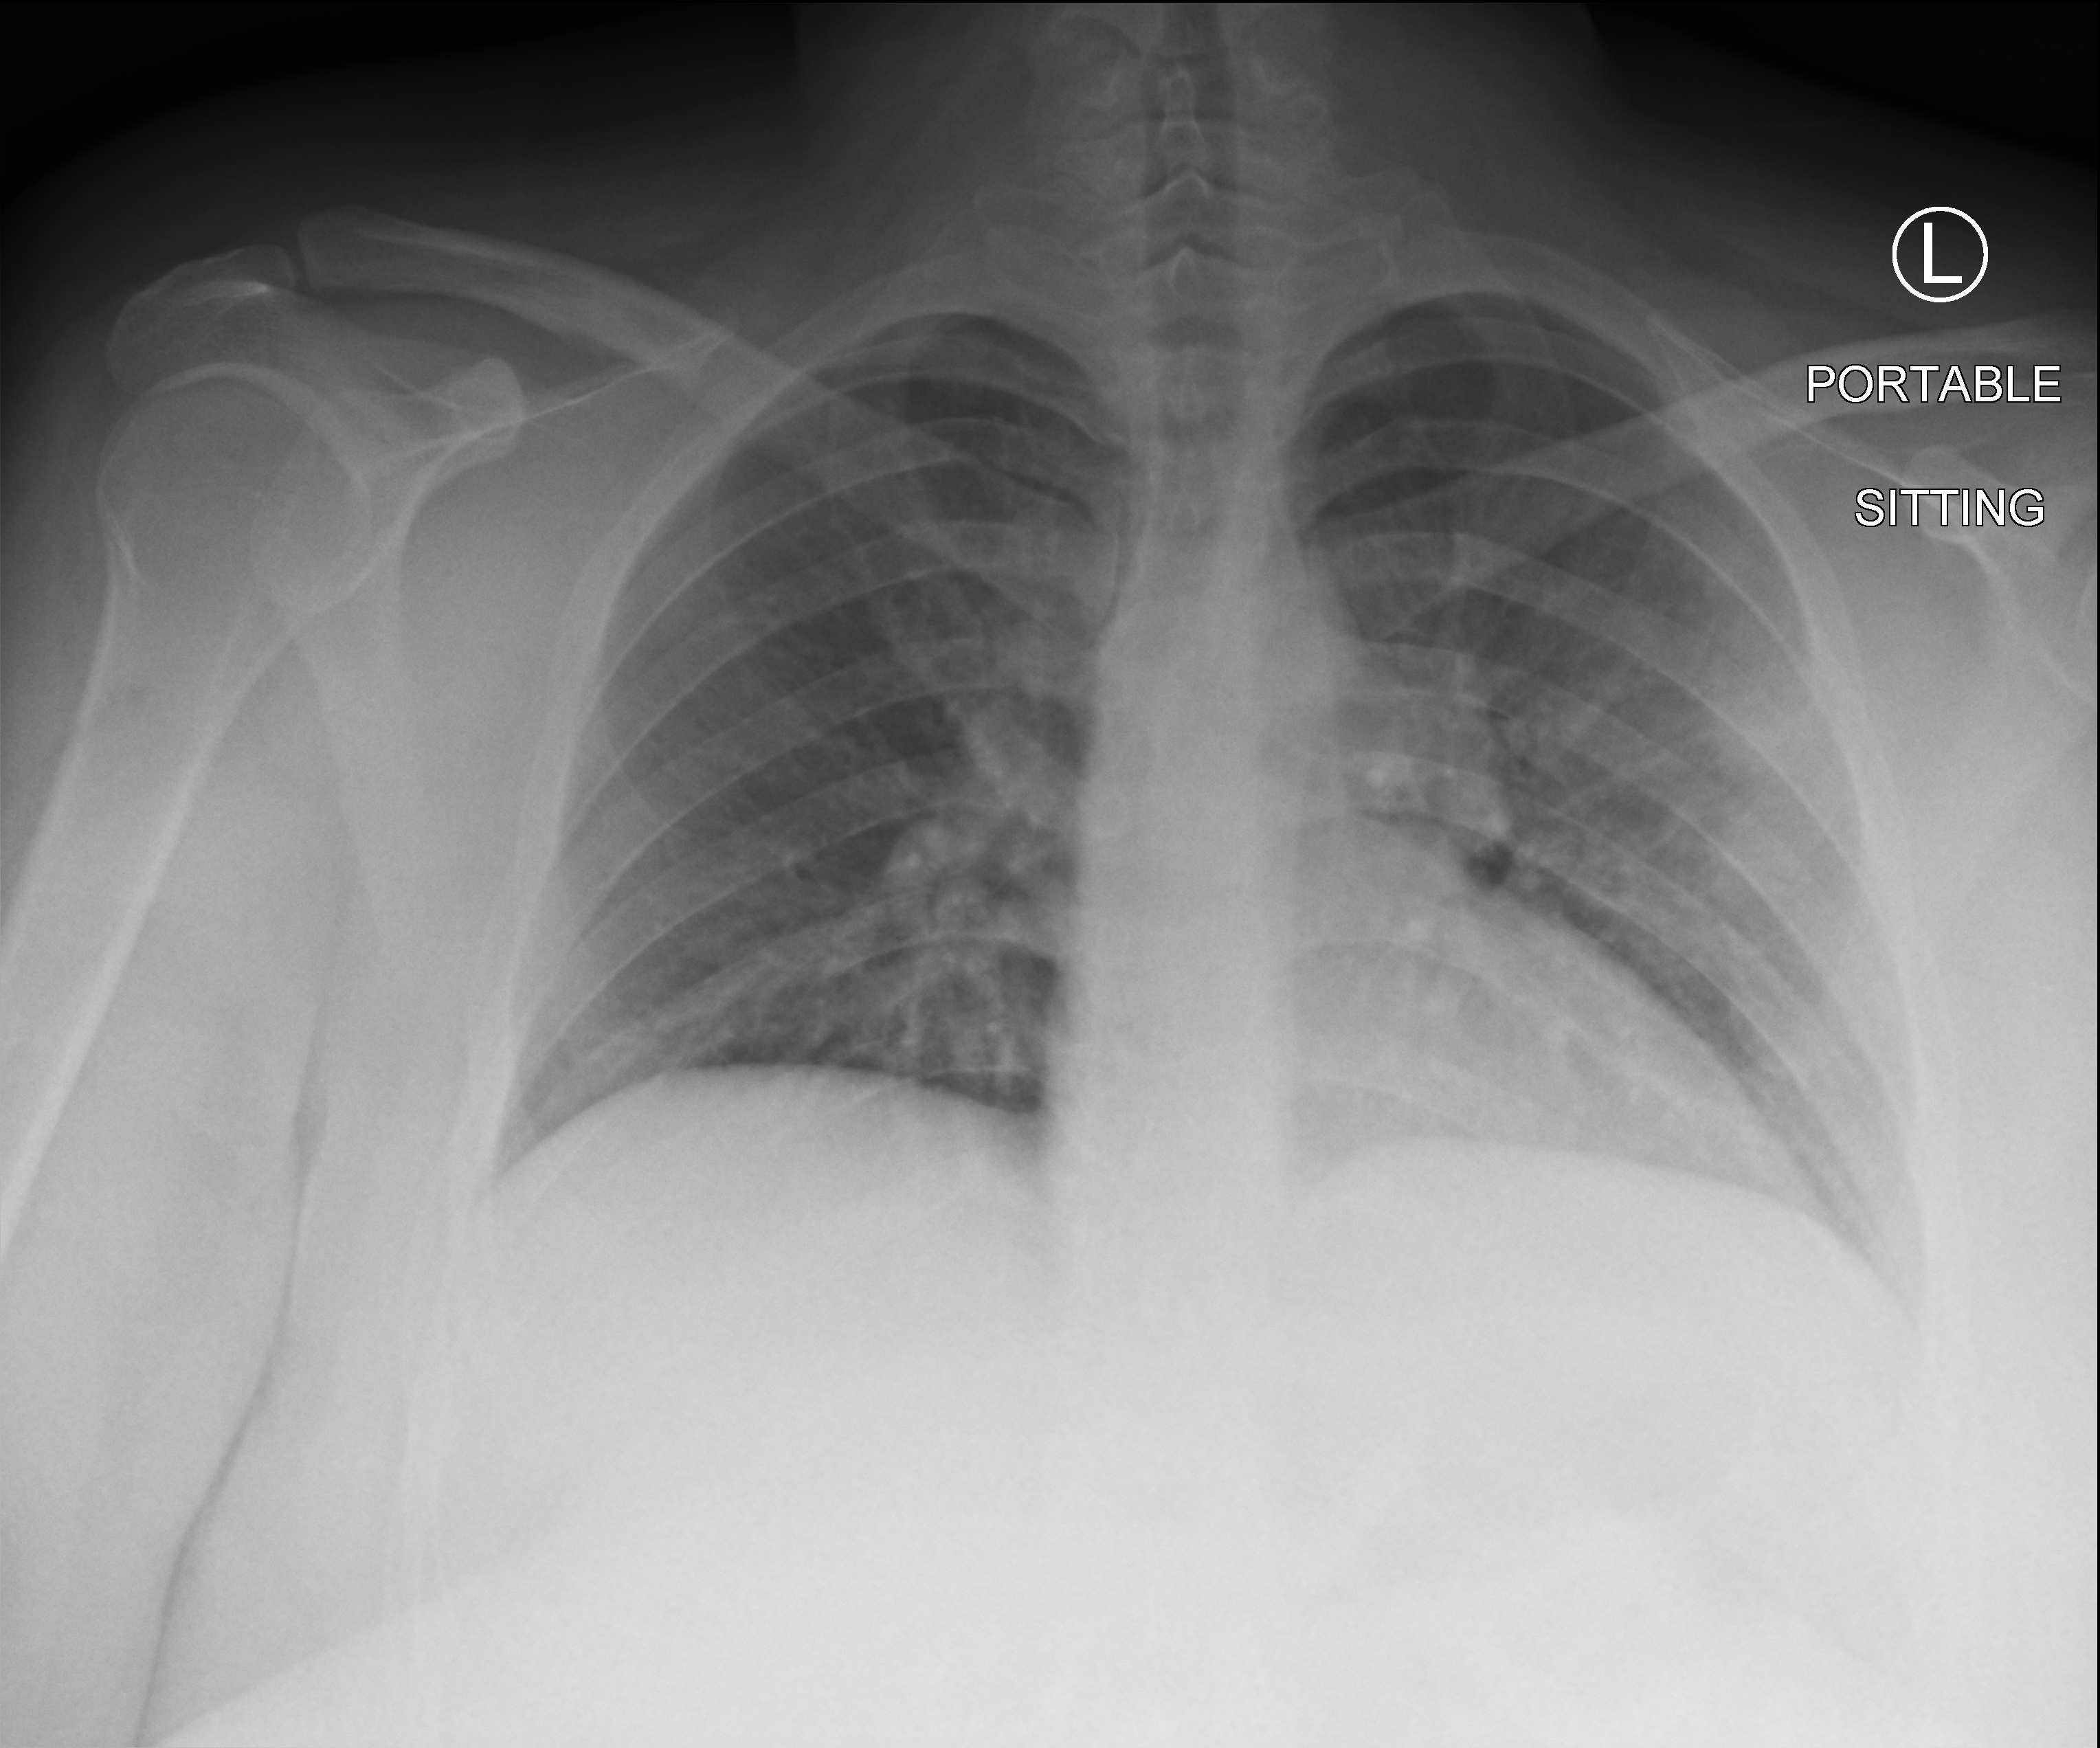
Portable chest radiograph; anteroposterior (AP) projection. Female patient hospitalised with COVID-19, age 18–59 years.
Admission-level facts for this patient (not findings on this image; timing relative to this image not recorded):
- mechanically ventilated during this hospital stay: no
- admitted to intensive care during this hospital stay: no
- length of hospital stay: 1 day